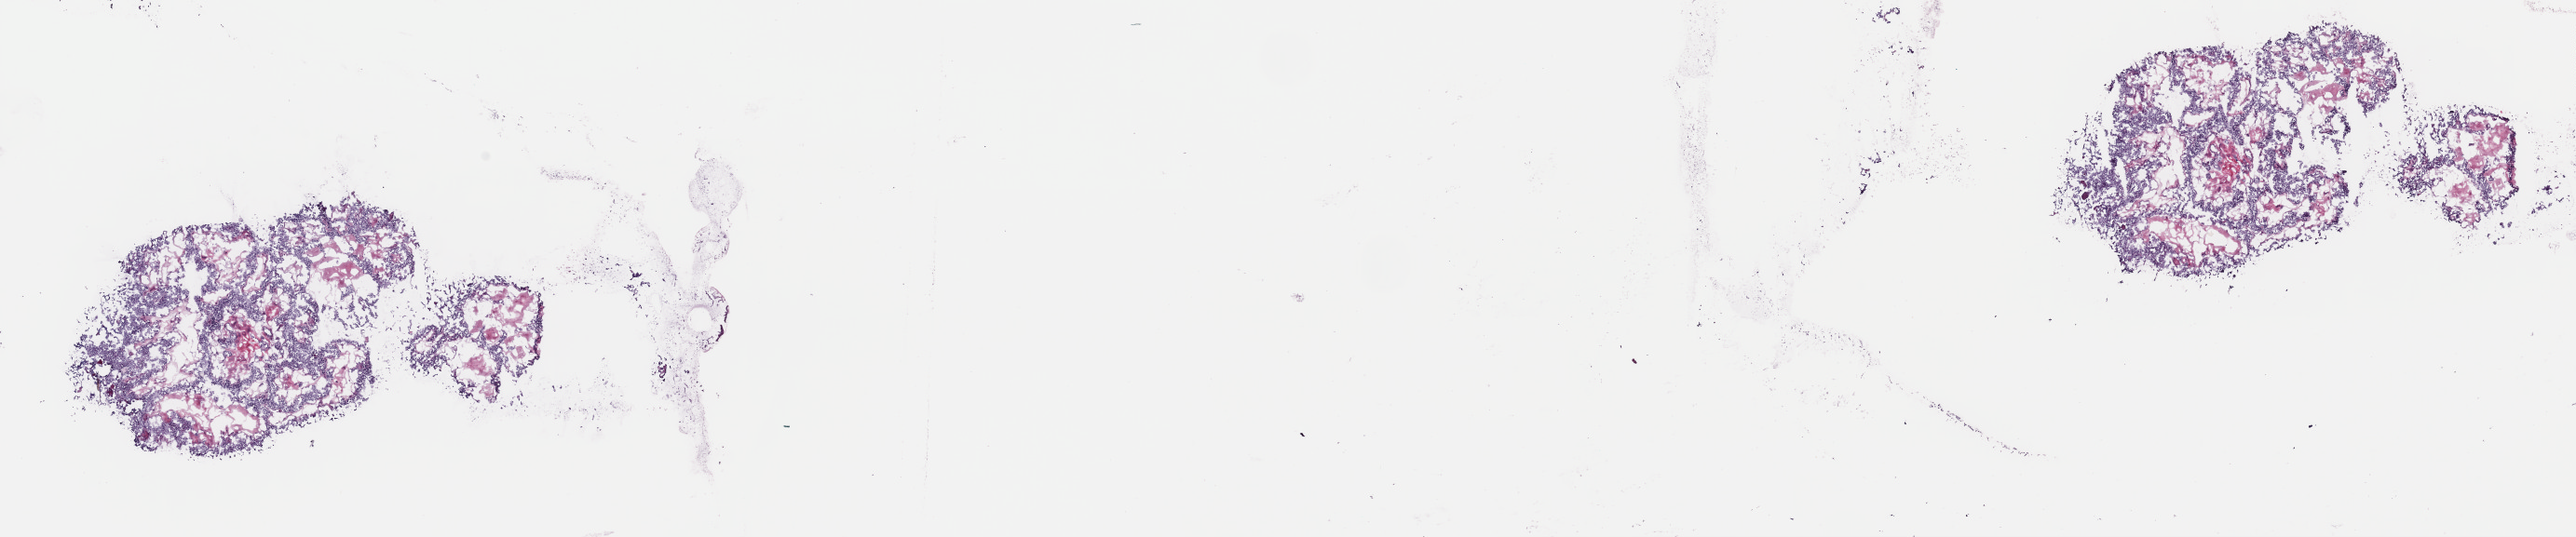
Digitized H&E tissue section (whole slide), shown as a low-resolution overview of the whole scanned area (about 21.9 x 4.6 mm), frozen section from the top of the tissue portion, sample: primary tumour, thyroid. Female, age 30 years at initial diagnosis. Composition of this section per pathologist review: tumour cells 60%, tumour nuclei 100%, normal cells 0%, stromal cells 40%, necrosis 0%. Inflammatory infiltration, as recorded: lymphocyte infiltration 1%, monocyte infiltration 0%, neutrophil infiltration 0%.
Lymph nodes positive (case pathology): 17 of 25 examined. Laterality: midline. Diagnosis: Papillary adenocarcinoma, NOS. AJCC pathologic stage: I (7th edition).